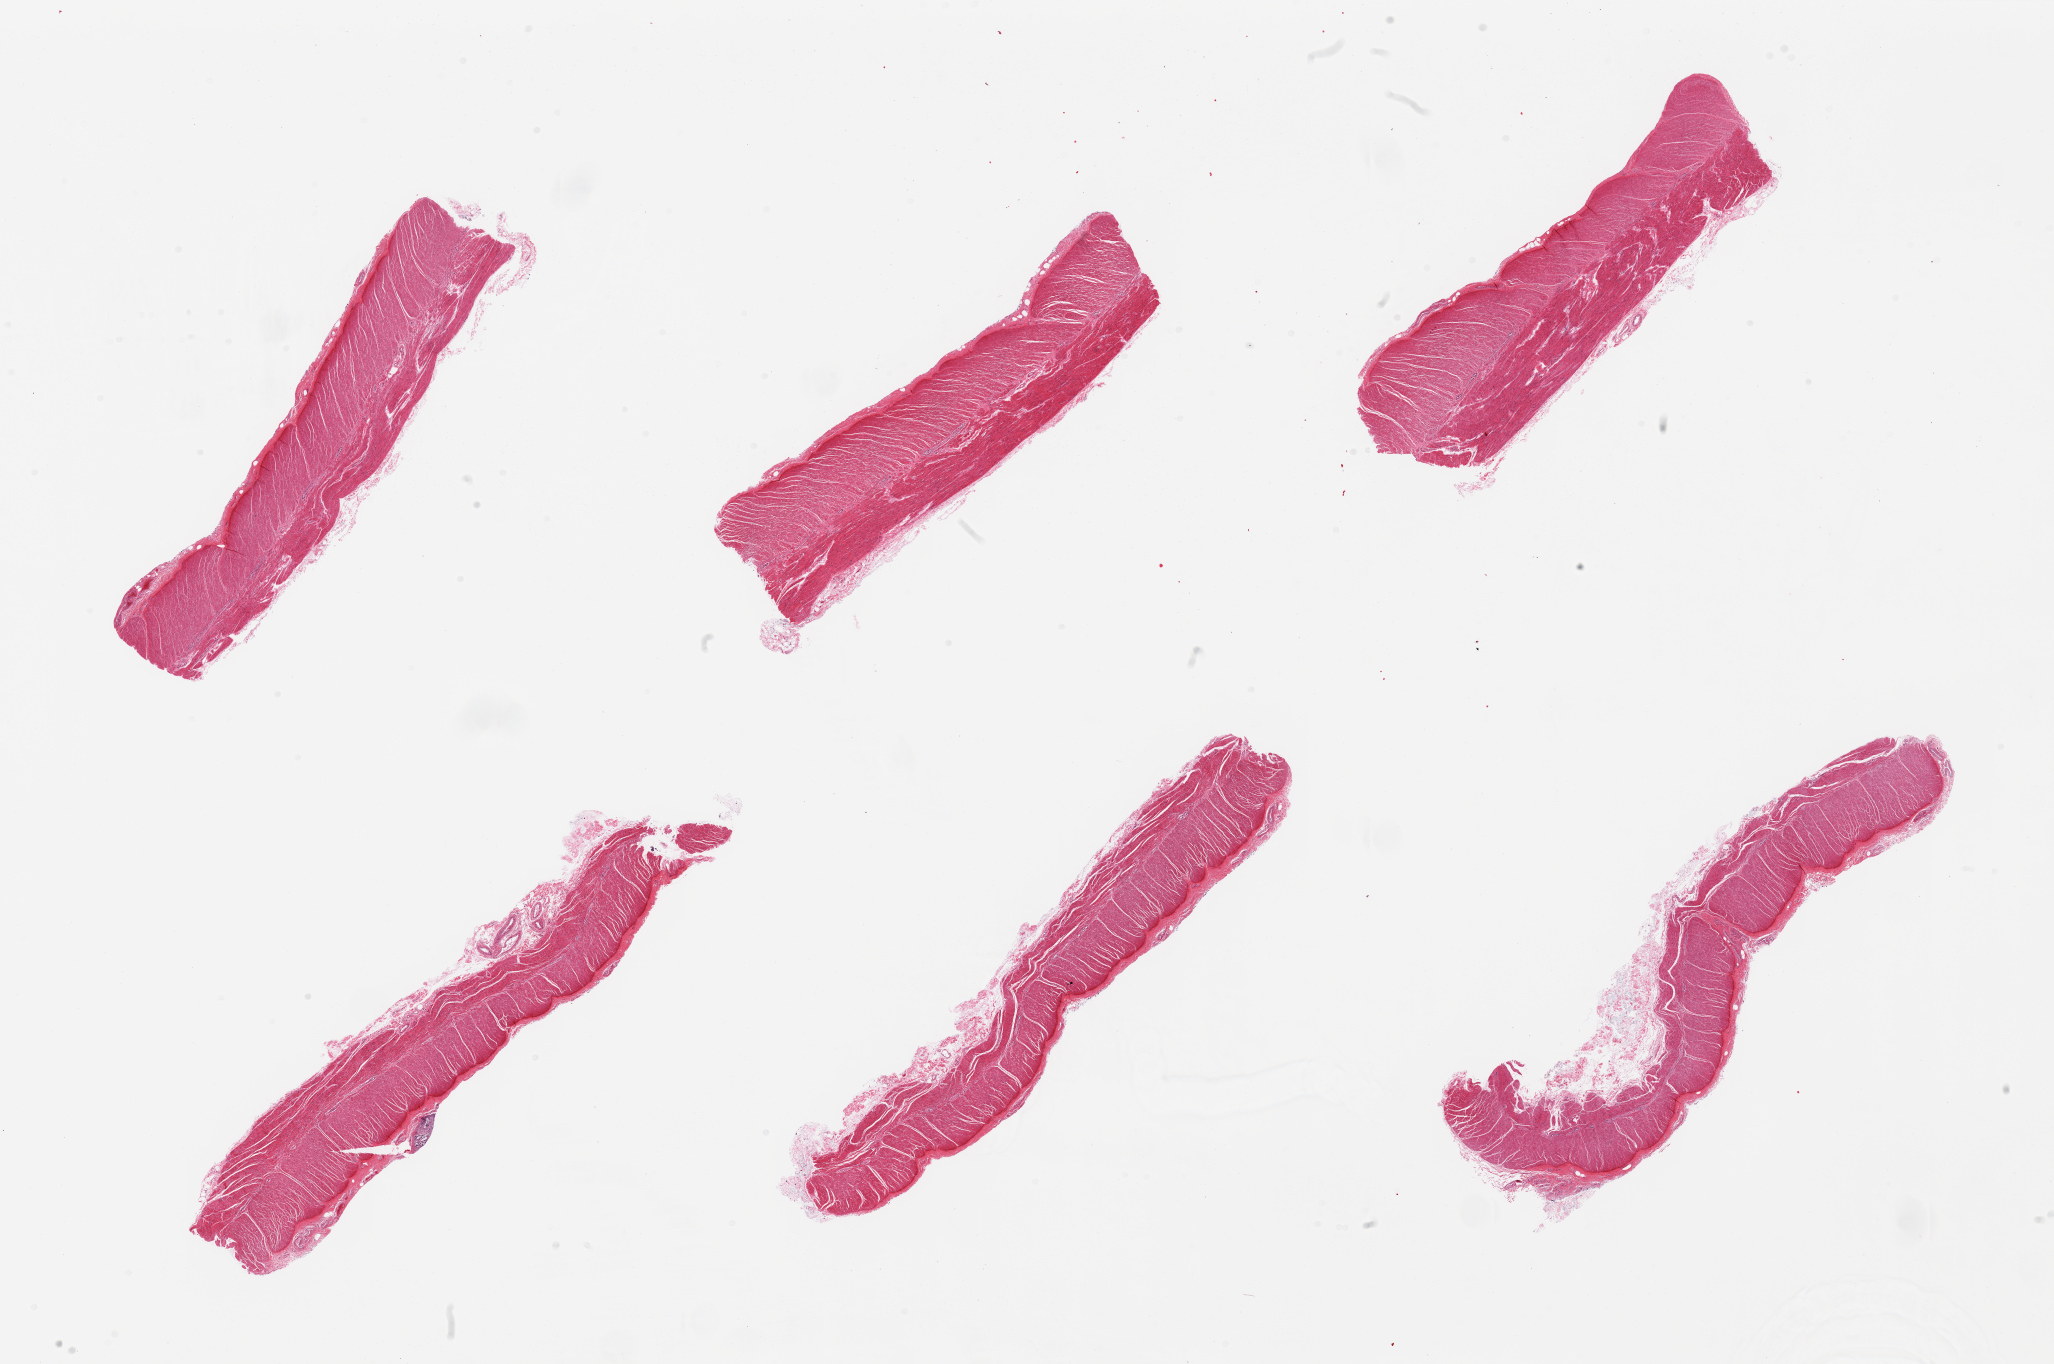
Whole-slide image, haematoxylin and eosin stain, brightfield, shown as a low-resolution overview of the whole scanned area (about 32.5 x 21.6 mm, acquisition: 20x scan). PAXgene-fixed paraffin-embedded (PFPE) section. Section of sigmoid colon (target tissue). Donor tissue sample.
- pathologist's review note for this sample: 6 pieces, well trimmed, small focus of autolyzed mucosa